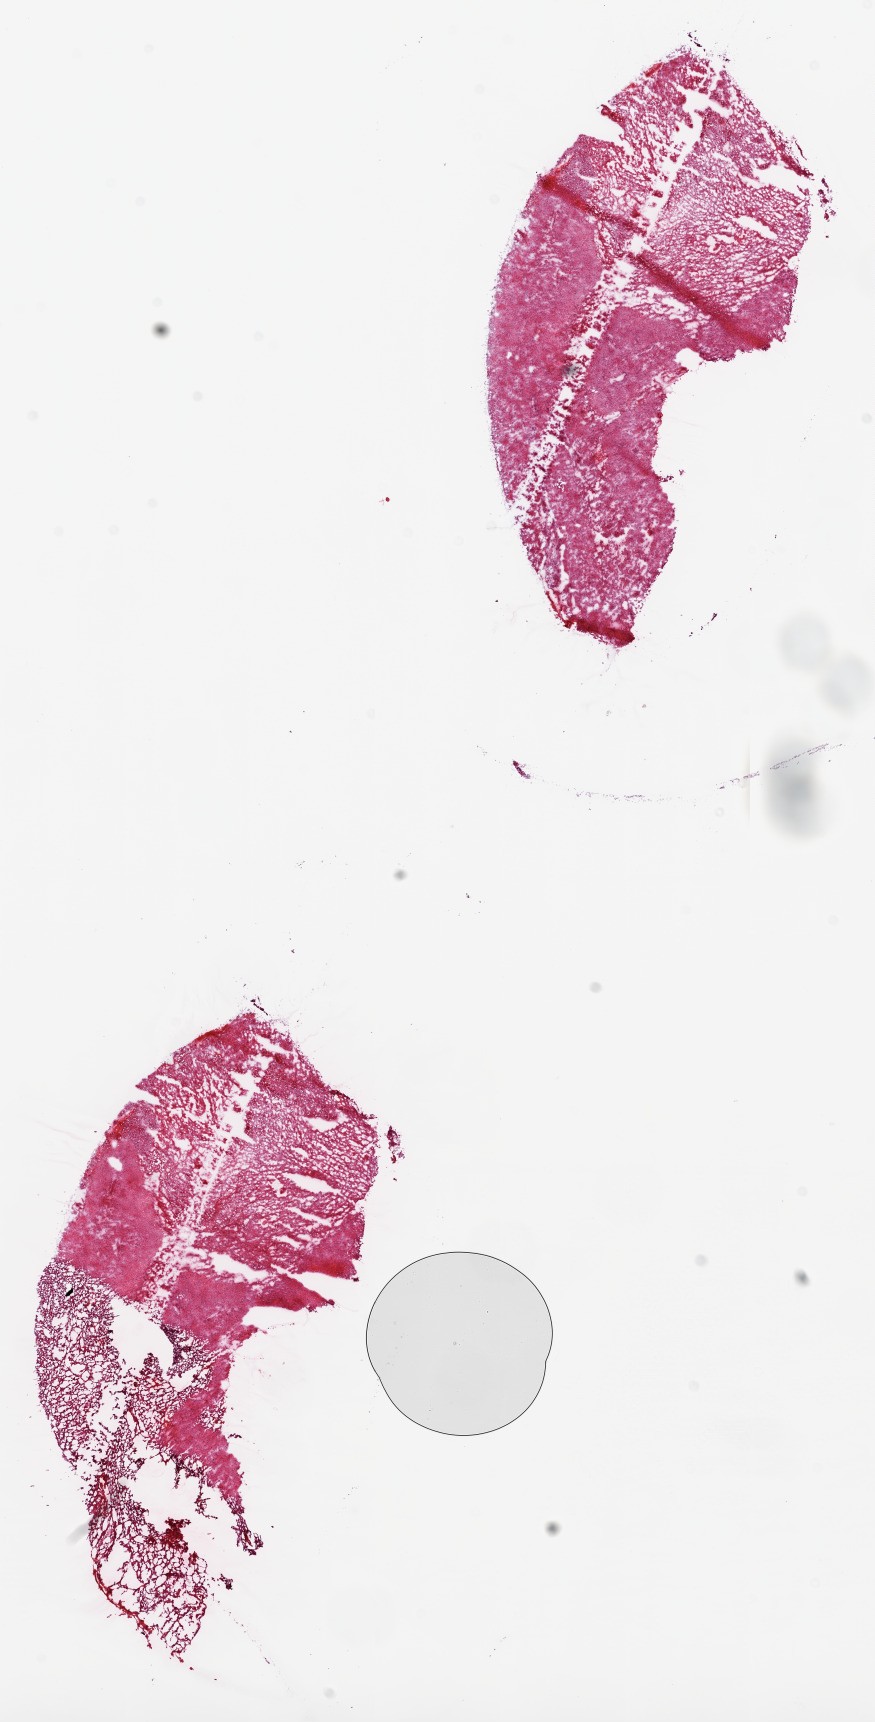
H&E-stained whole-slide image, a low-resolution overview of the entire scanned area, about 7.0 x 13.8 mm, frozen section, brain, primary tumour sample. Patient: female, age at initial diagnosis 66 years. Pathologist review of this section (percent, as recorded): tumour cells 60%, tumour nuclei 95%, normal cells 0%, necrosis 40%.
Histologic diagnosis: Glioblastoma.